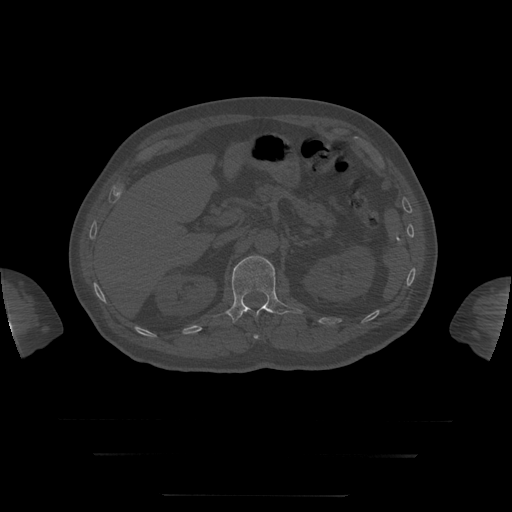
CT including the spine, one axial slice; position 53 of 397 along the scan axis; reconstruction kernel STANDARD; bone window (W 1800 / L 400 HU); 512 × 512 image matrix. Patient age 73 years. Case-level facts recorded for this patient, not image findings: primary cancer: prostate.
Structures marked on this image (semi-automatic segmentation, software-assisted and operator-edited):
- L1 vertebra: box from (x=227, y=256) to (x=303, y=323) px
- T12 vertebra: (x=254, y=335)–(x=259, y=339)
- T8 vertebra: (x=234, y=300)–(x=273, y=323)